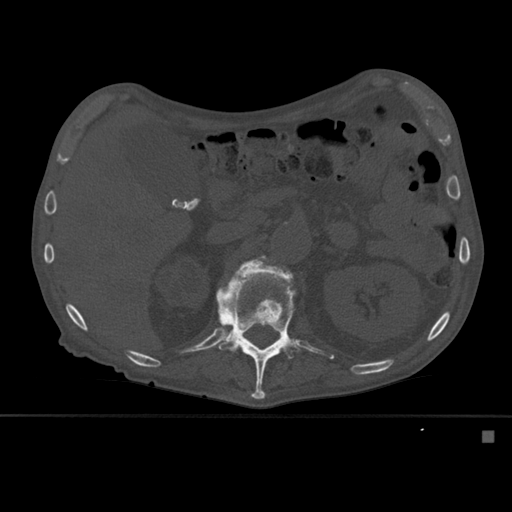
CT including the spine, one axial slice; position 256 of 527 along the scan axis; bone window (W 1800 / L 400 HU); 1.5 mm slice thickness; 512 × 512 image matrix, field of view 373 × 373 mm. Male patient, age 78 years. From the clinical record (not read from this slice): primary cancer: prostate.
Outlined on this slice (semi-automatic segmentation, software-assisted and operator-edited):
- L1 vertebra: bounding box [x1, y1, x2, y2] px = [216, 260, 300, 400]